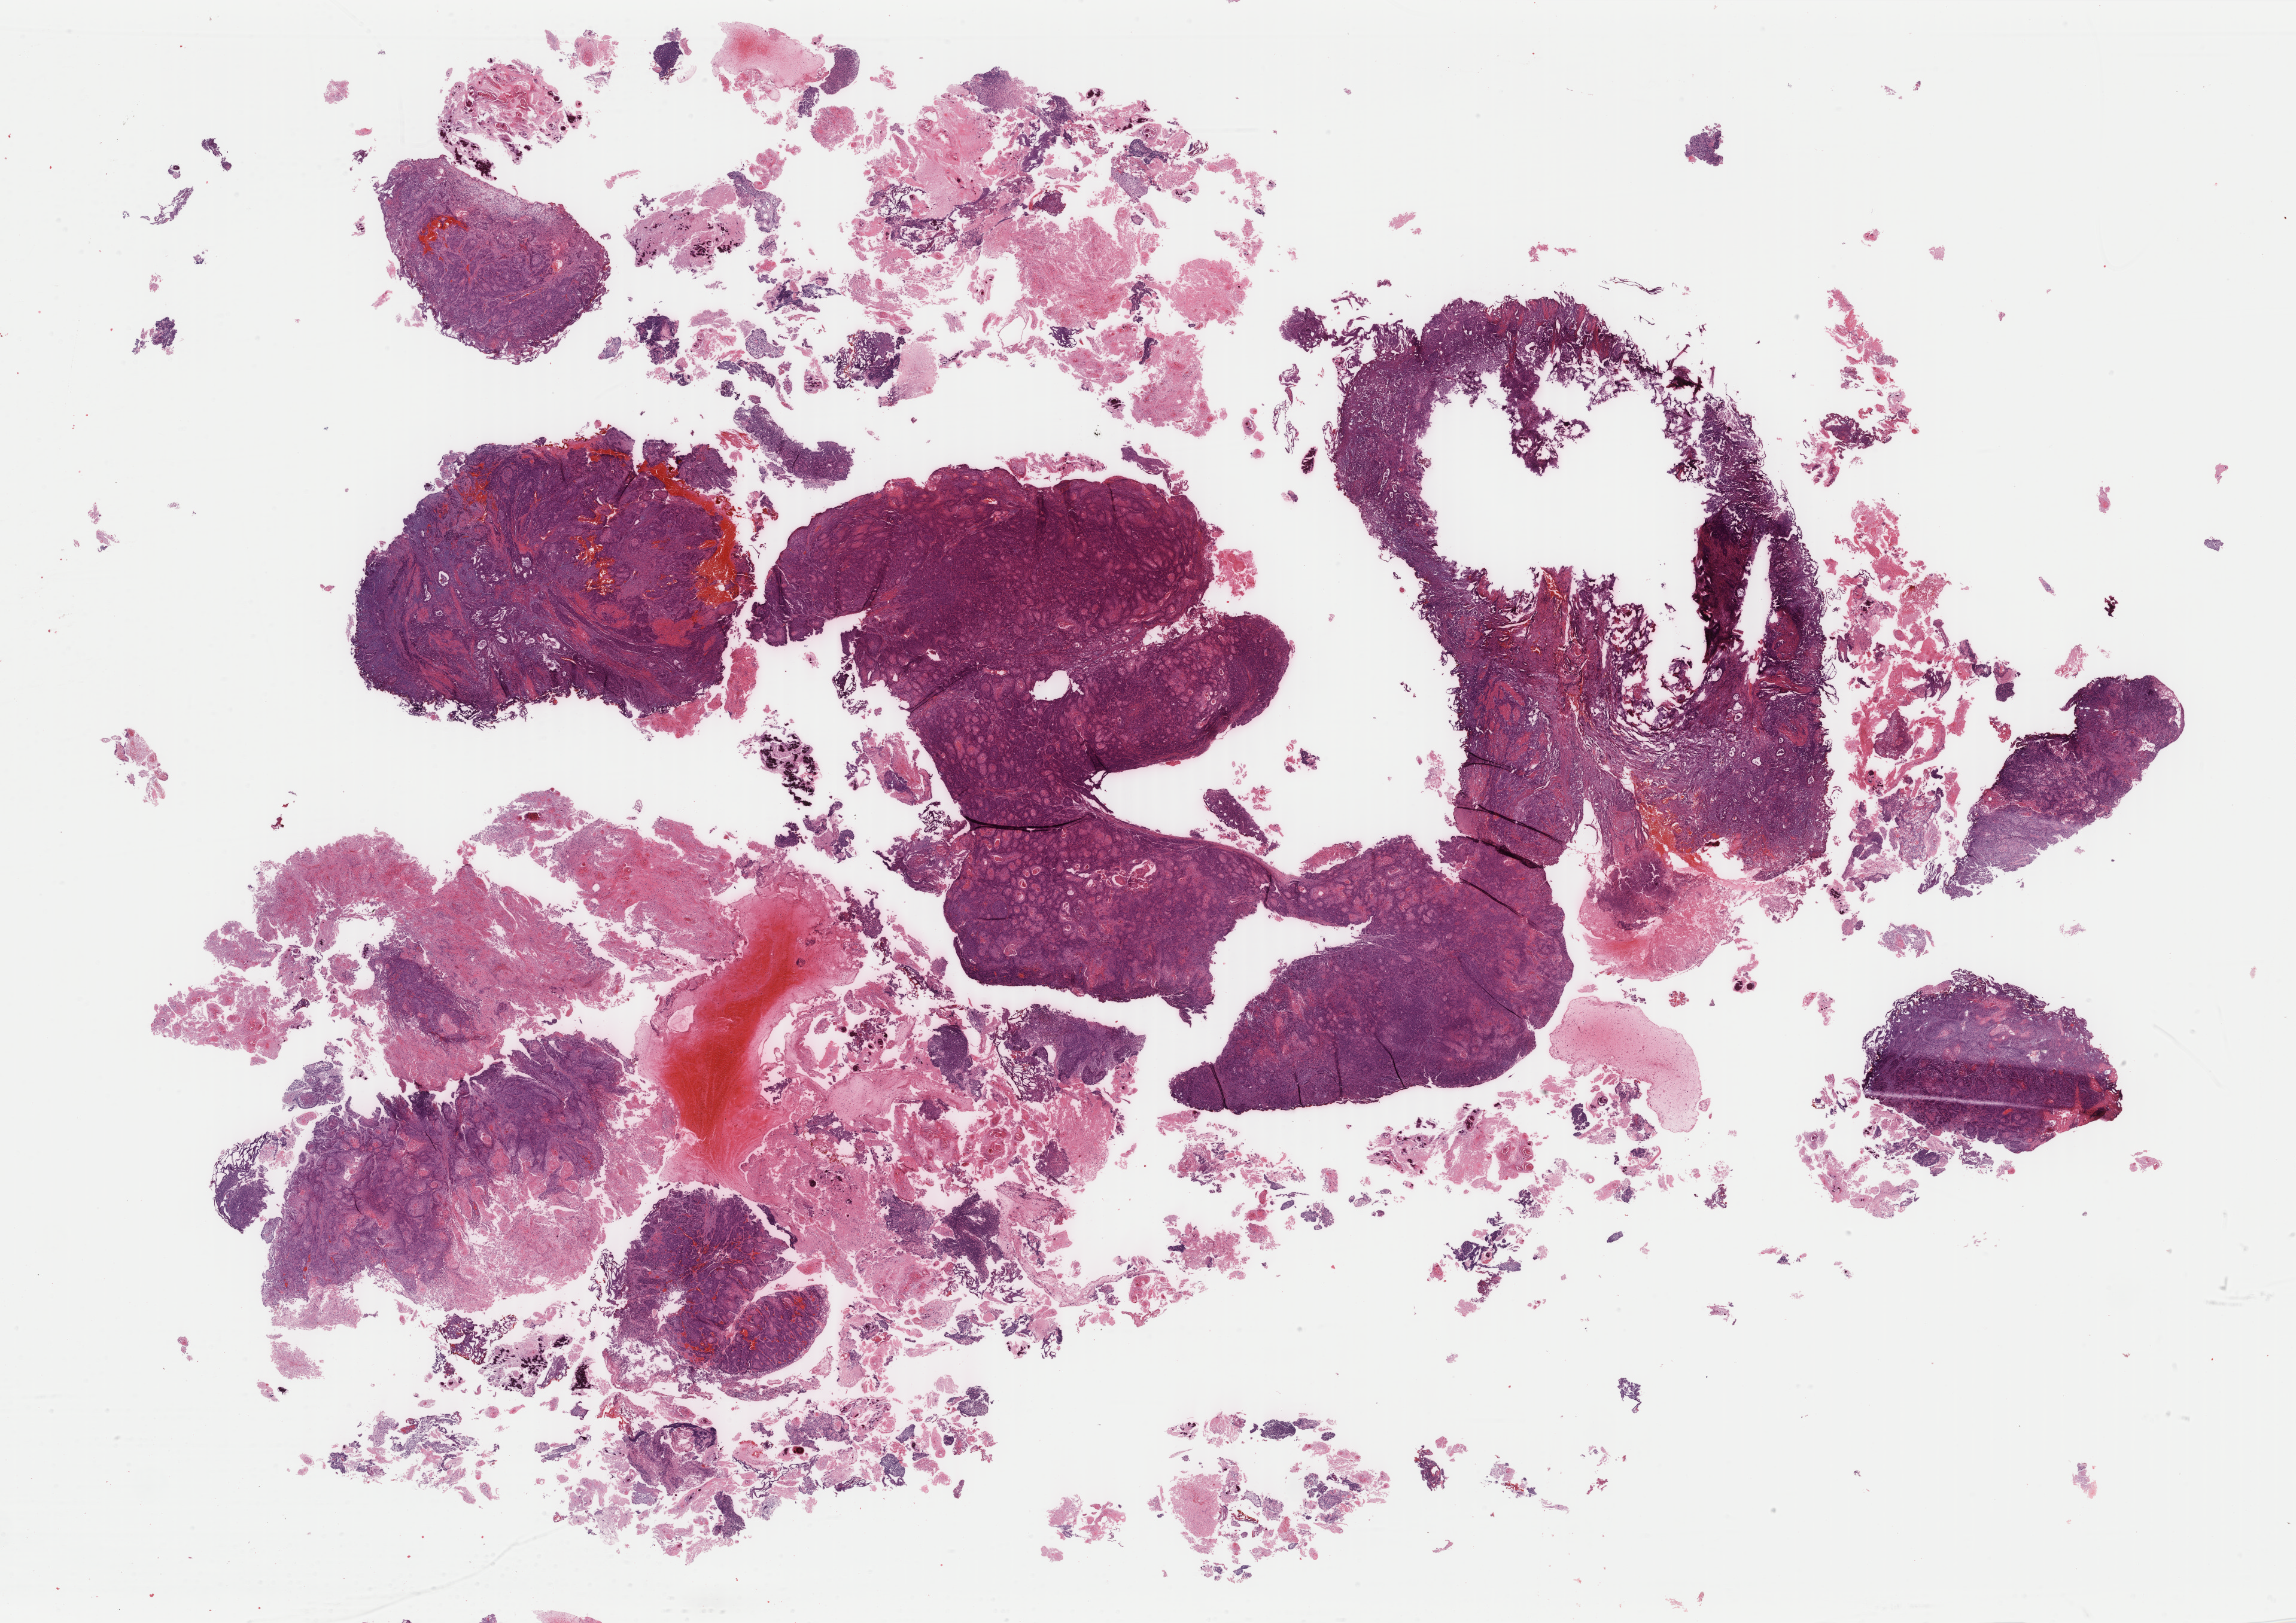
H&E whole-slide image, shown as a low-resolution overview of the whole scanned area (about 30.5 x 21.5 mm); formalin-fixed paraffin-embedded (FFPE) diagnostic section; bladder, primary tumour sample. Patient: male, age at initial diagnosis 66 years. Histologic grade: high grade.
Pathologic diagnosis: Transitional cell carcinoma. AJCC pathologic stage: II (6th edition).